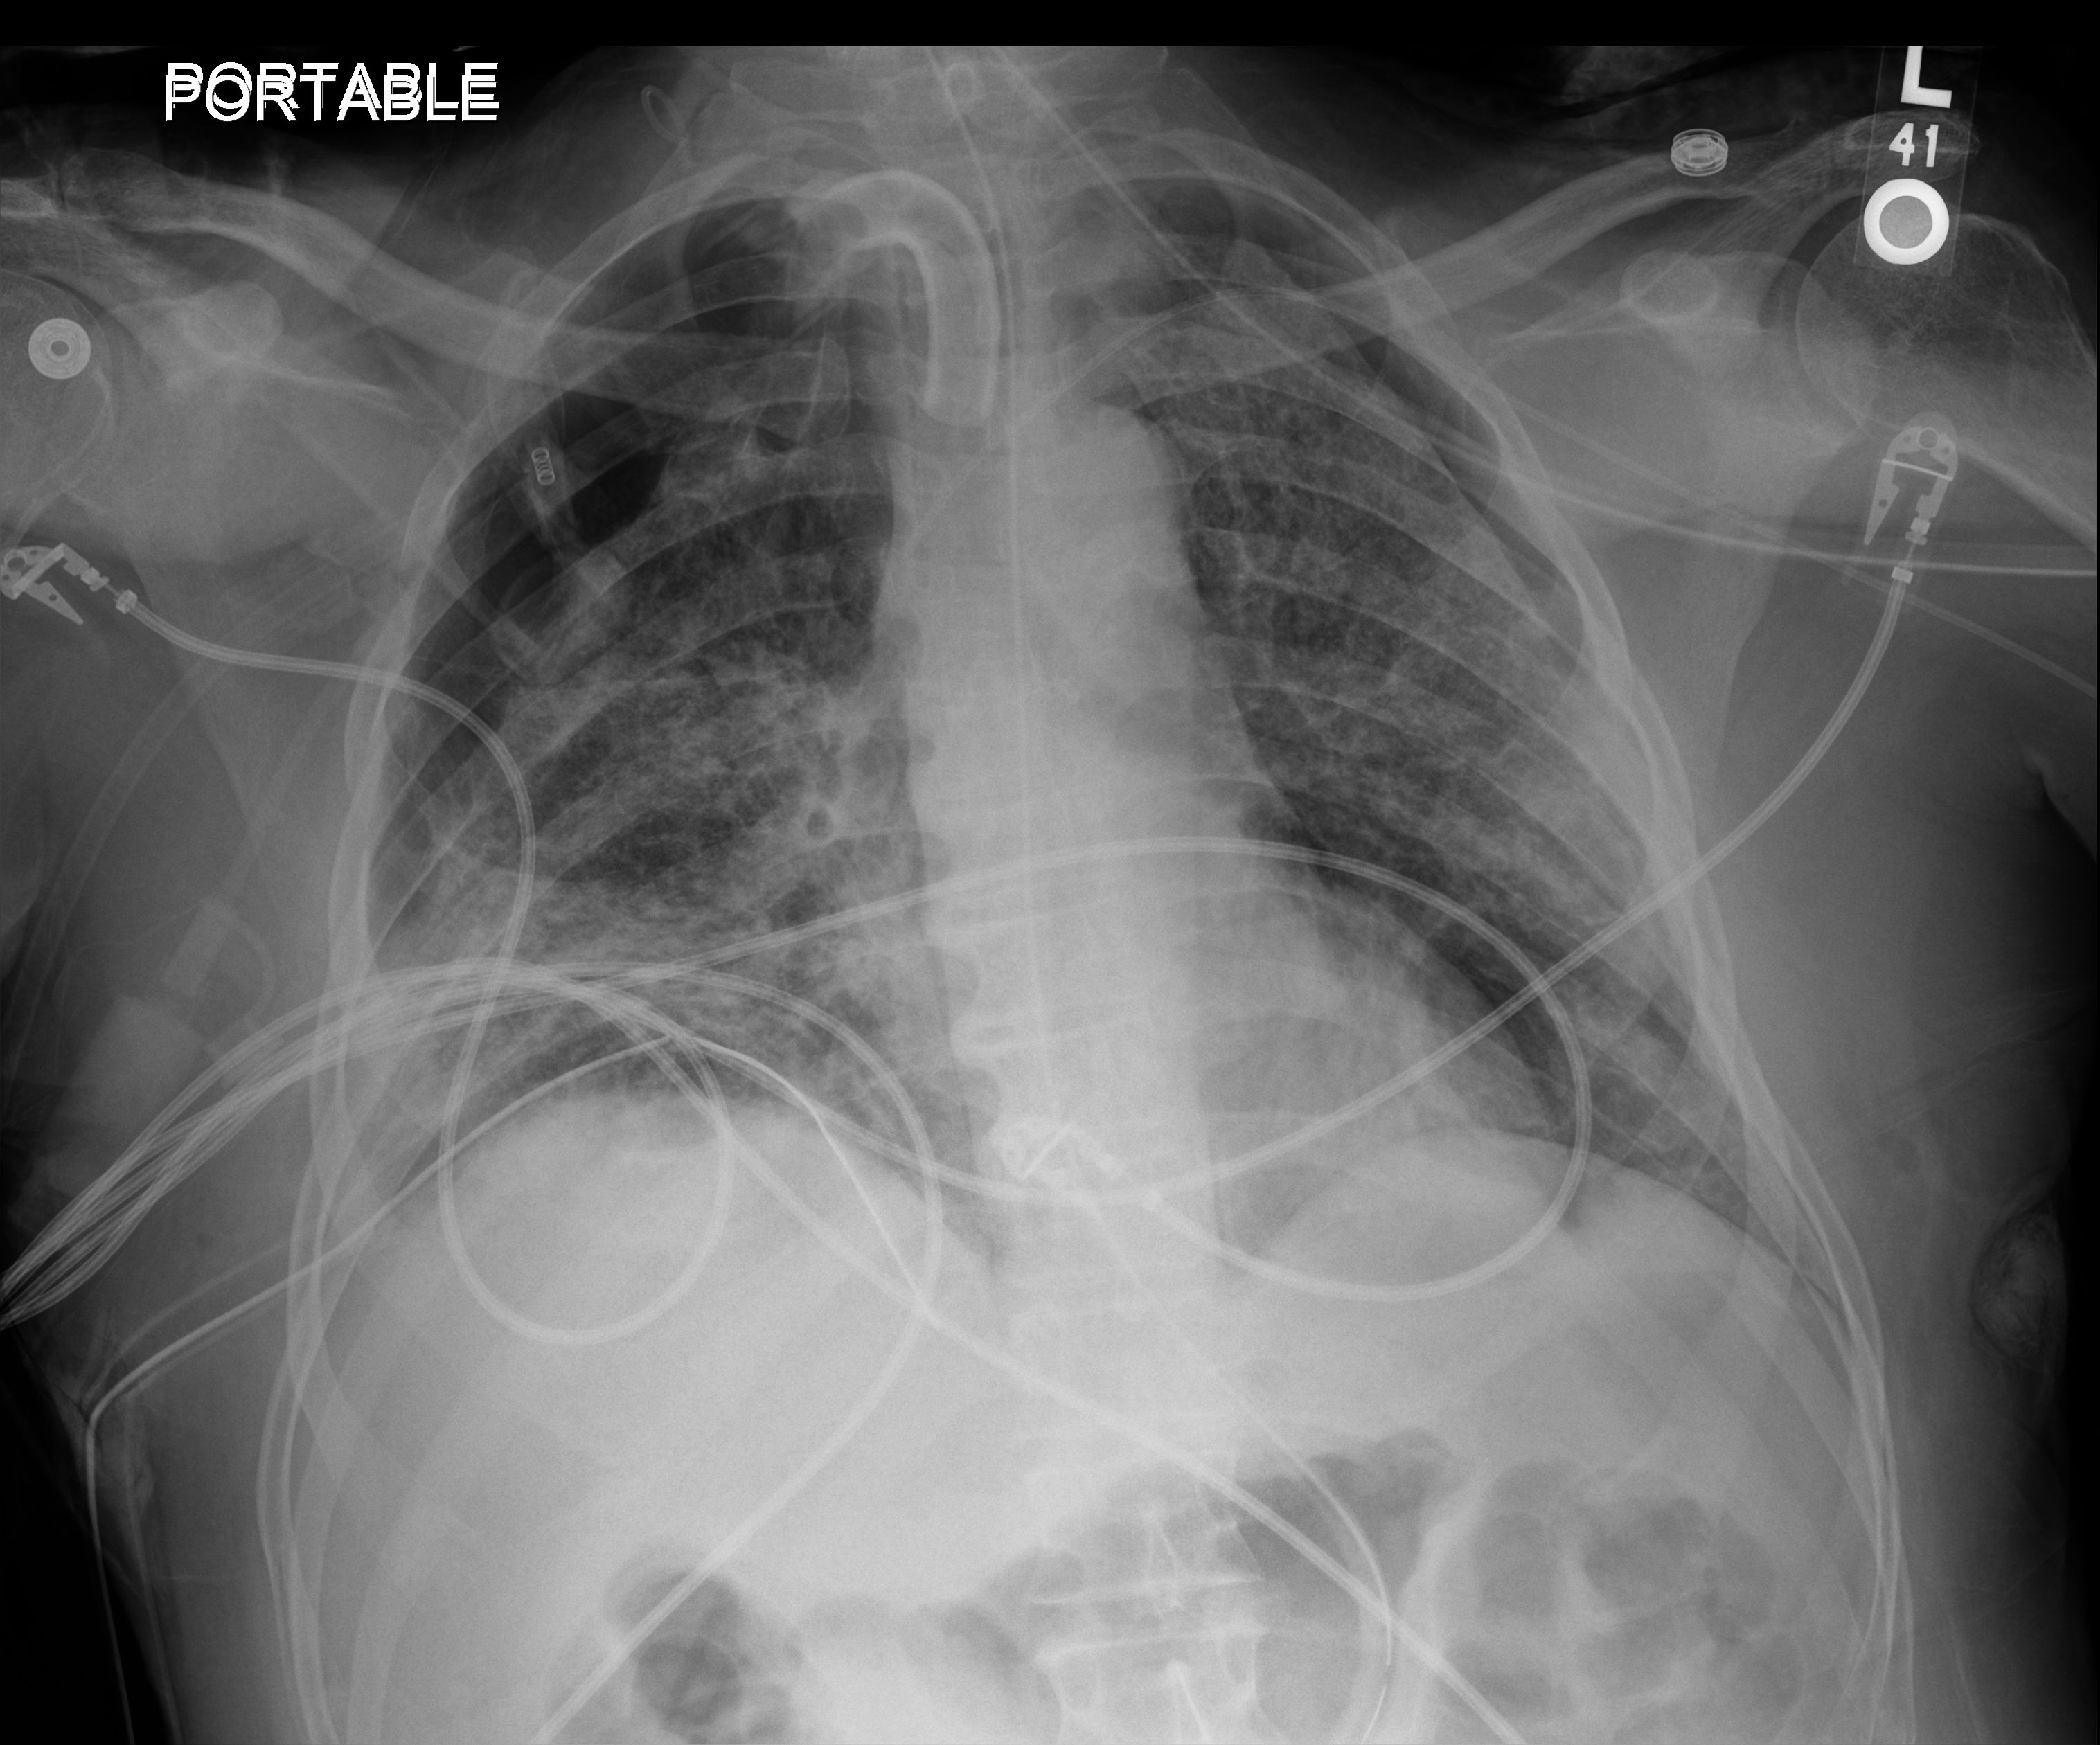
Chest X-ray (portable), anteroposterior (AP) projection. Patient hospitalised with COVID-19; male, aged 18–59 years.
Hospital-stay facts (about this admission, not read from this image; timing relative to this image not recorded):
- mechanically ventilated during this hospital stay: yes
- admitted to intensive care during this hospital stay: yes